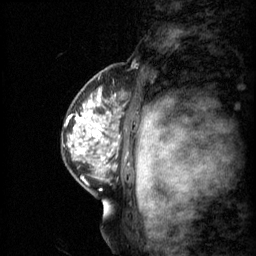
Breast MRI (dynamic contrast-enhanced), one sagittal slice; position 45 of 60 along the scan axis; 3 images stored at this slice position (order not interpretable as contrast timing); 1.5 T; TE 4.2 ms, TR 11 ms; 2 mm slice thickness; 256 × 256 image matrix, field of view 200 × 200 mm. Female patient, age 48 years.
Annotated regions visible in this slice (semi-automatically segmented with operator editing):
- analysis volume of interest (the breast-tissue region the enhancement analysis was run in; not a lesion): bounding box (x1, y1, x2, y2) in pixels: (69, 74, 139, 147)
- tumour enhancement mask (voxels above the 70 % enhancement threshold inside the analysis volume of interest): (69, 90, 121, 147)